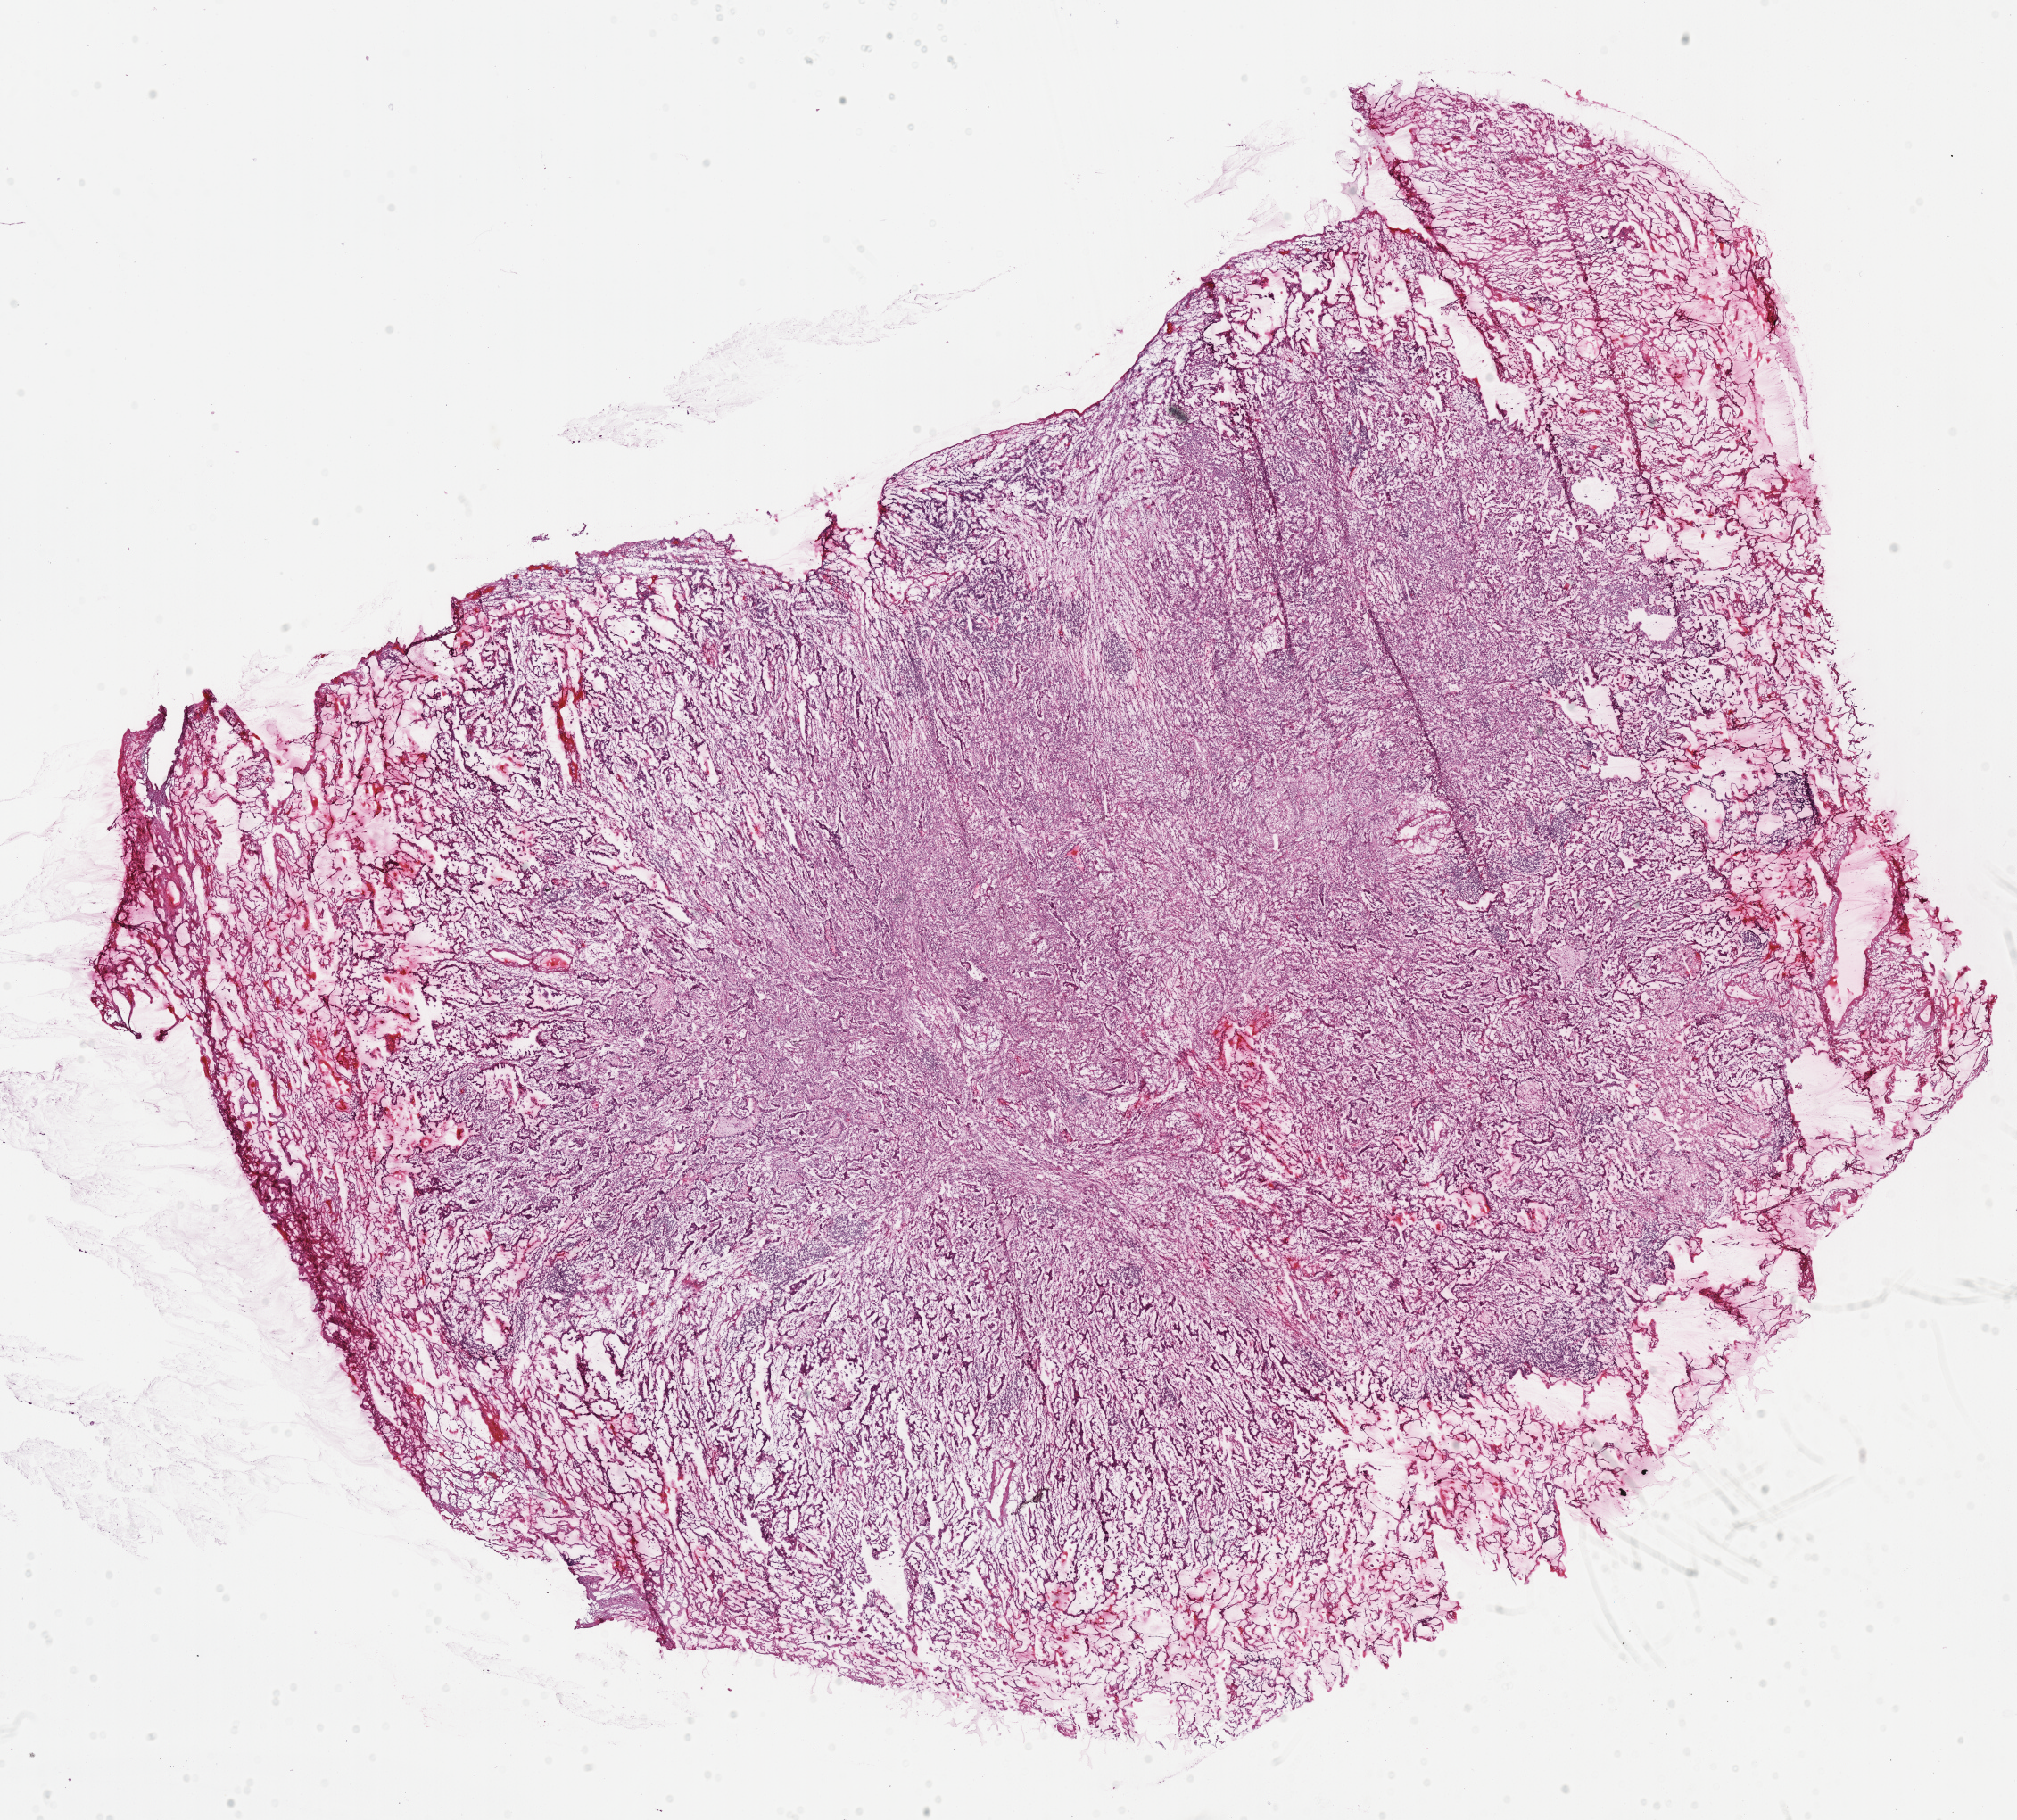
Whole-slide histology image, H&E-stained — low-resolution overview of the scanned area, about 17.8 x 16.1 mm, frozen section, sample: primary tumour, lung. Patient: female, age at initial diagnosis 76 years. Pathologist review of this section (percent, as recorded): tumour cells 75%, tumour nuclei 60%.
Pathologic diagnosis: Adenocarcinoma, NOS (upper lobe, lung).